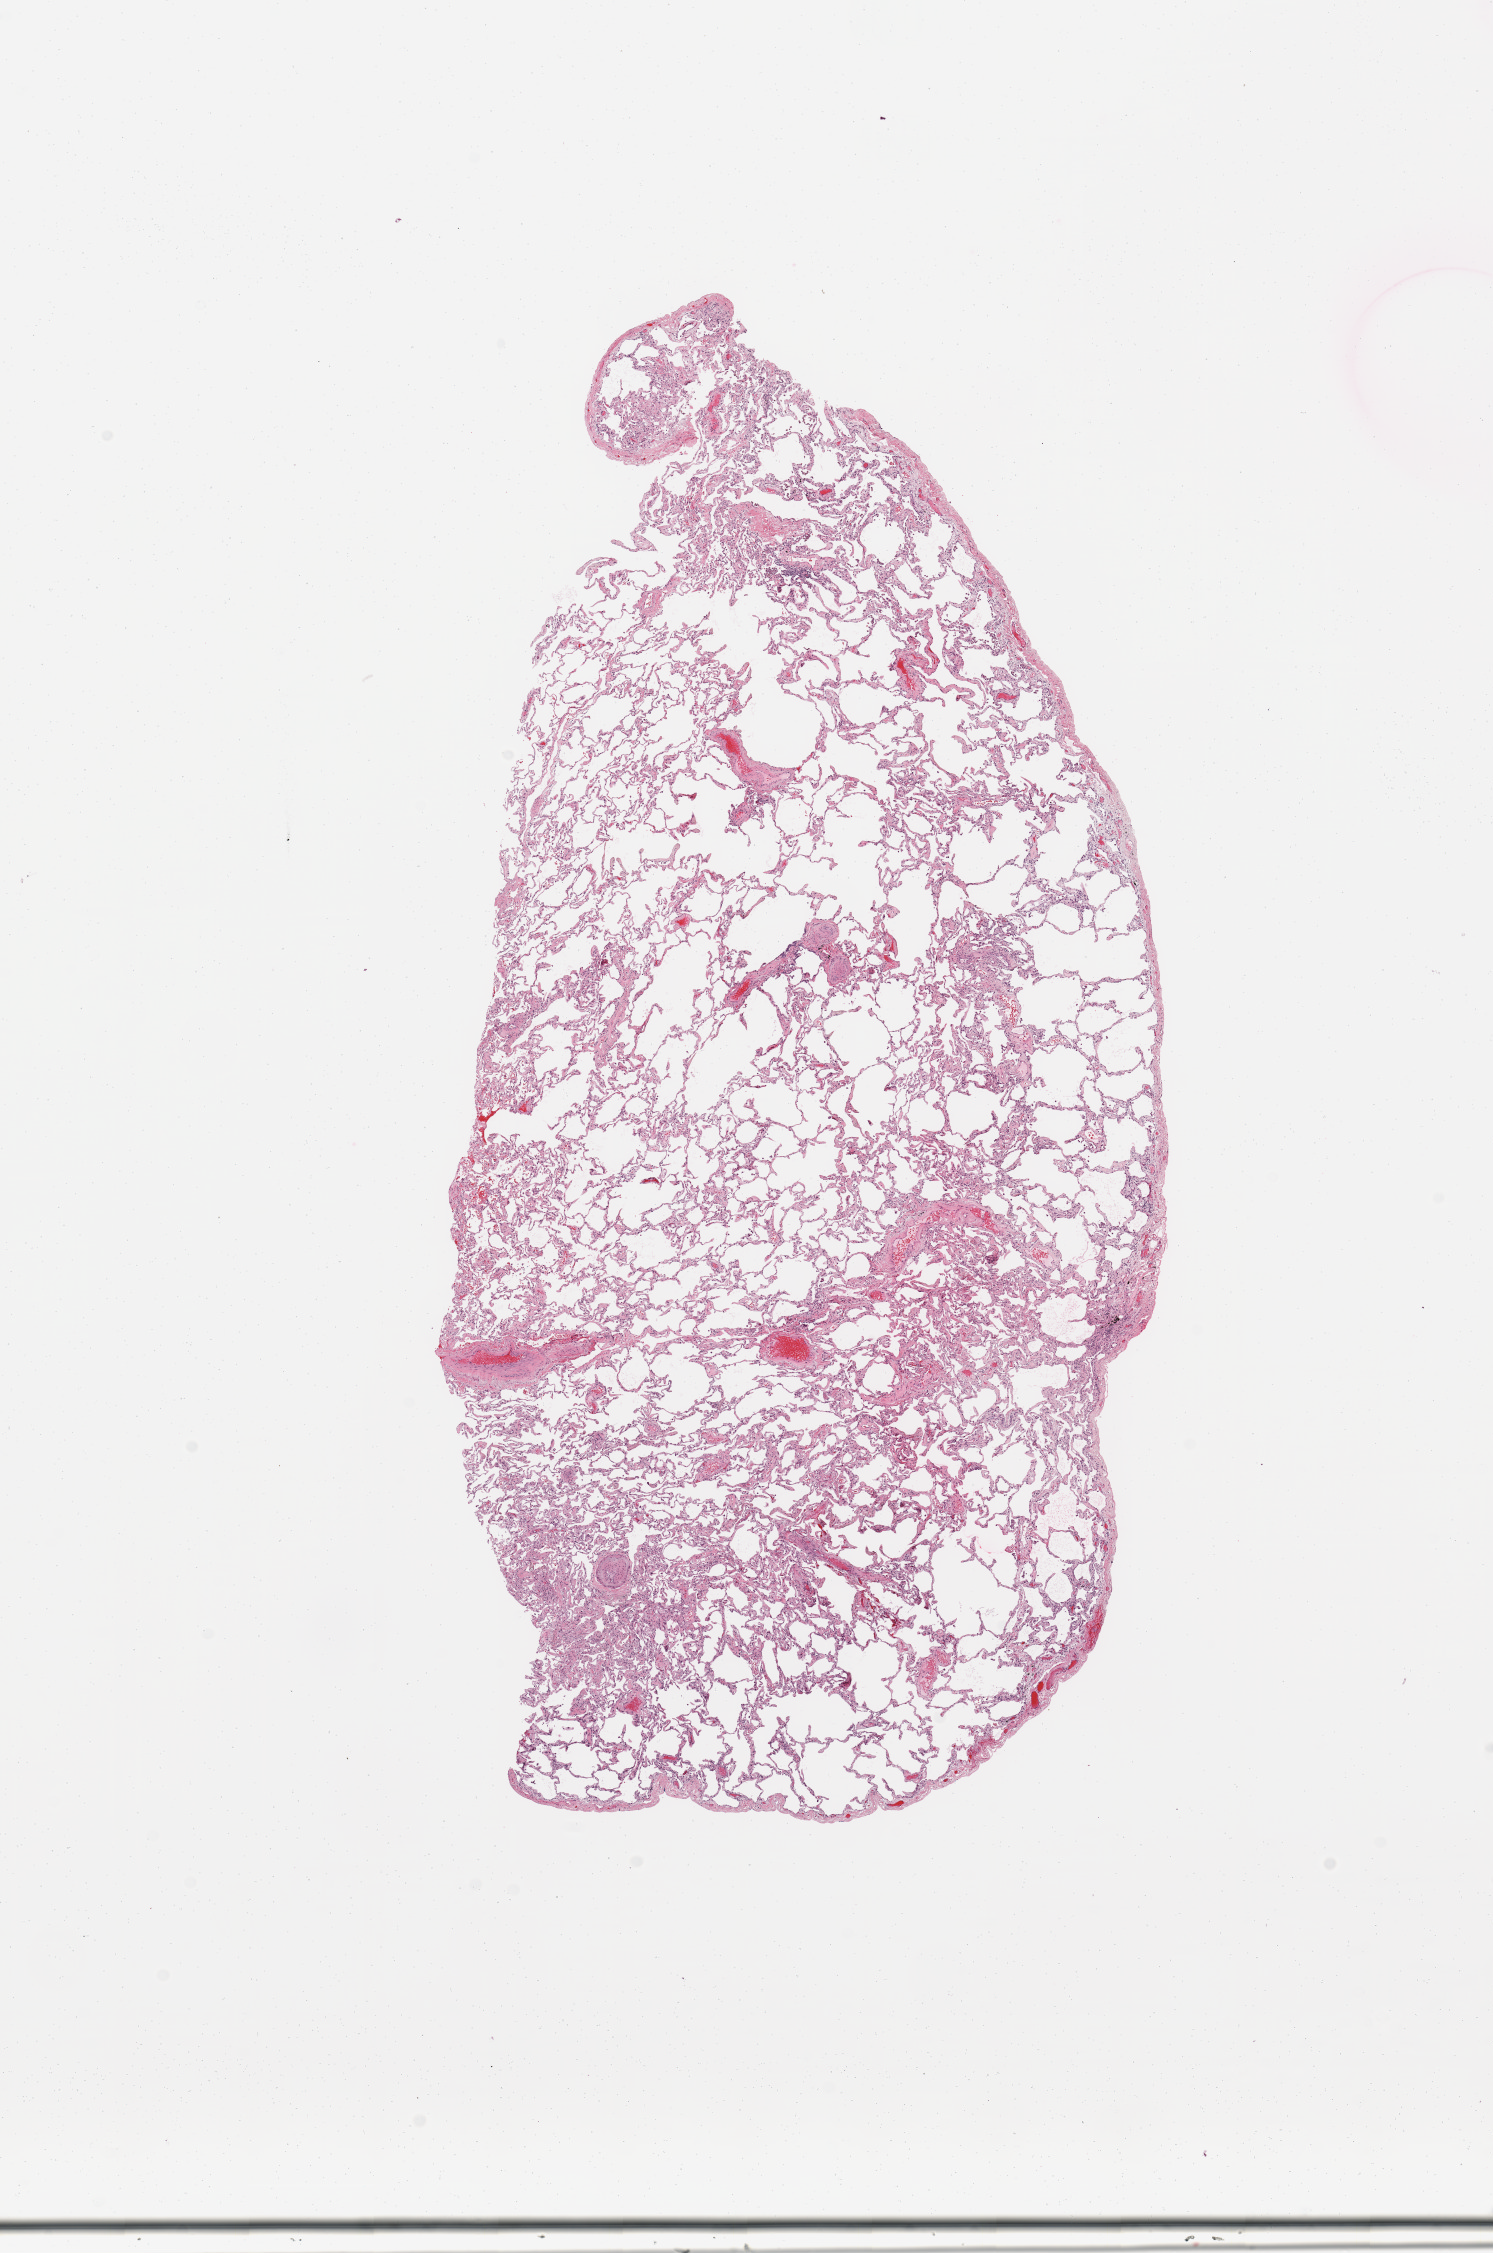
Digitized H&E-stained tissue section (whole slide), low-resolution overview of the scanned area, about 11.8 x 17.8 mm (from a 20x scan); normal (non-tumour) tissue sample, sampled site: lung. 71-year-old female patient.
- this section: normal (non-tumour) tissue from the same patient
- patient diagnosis: Adenocarcinoma, NOS